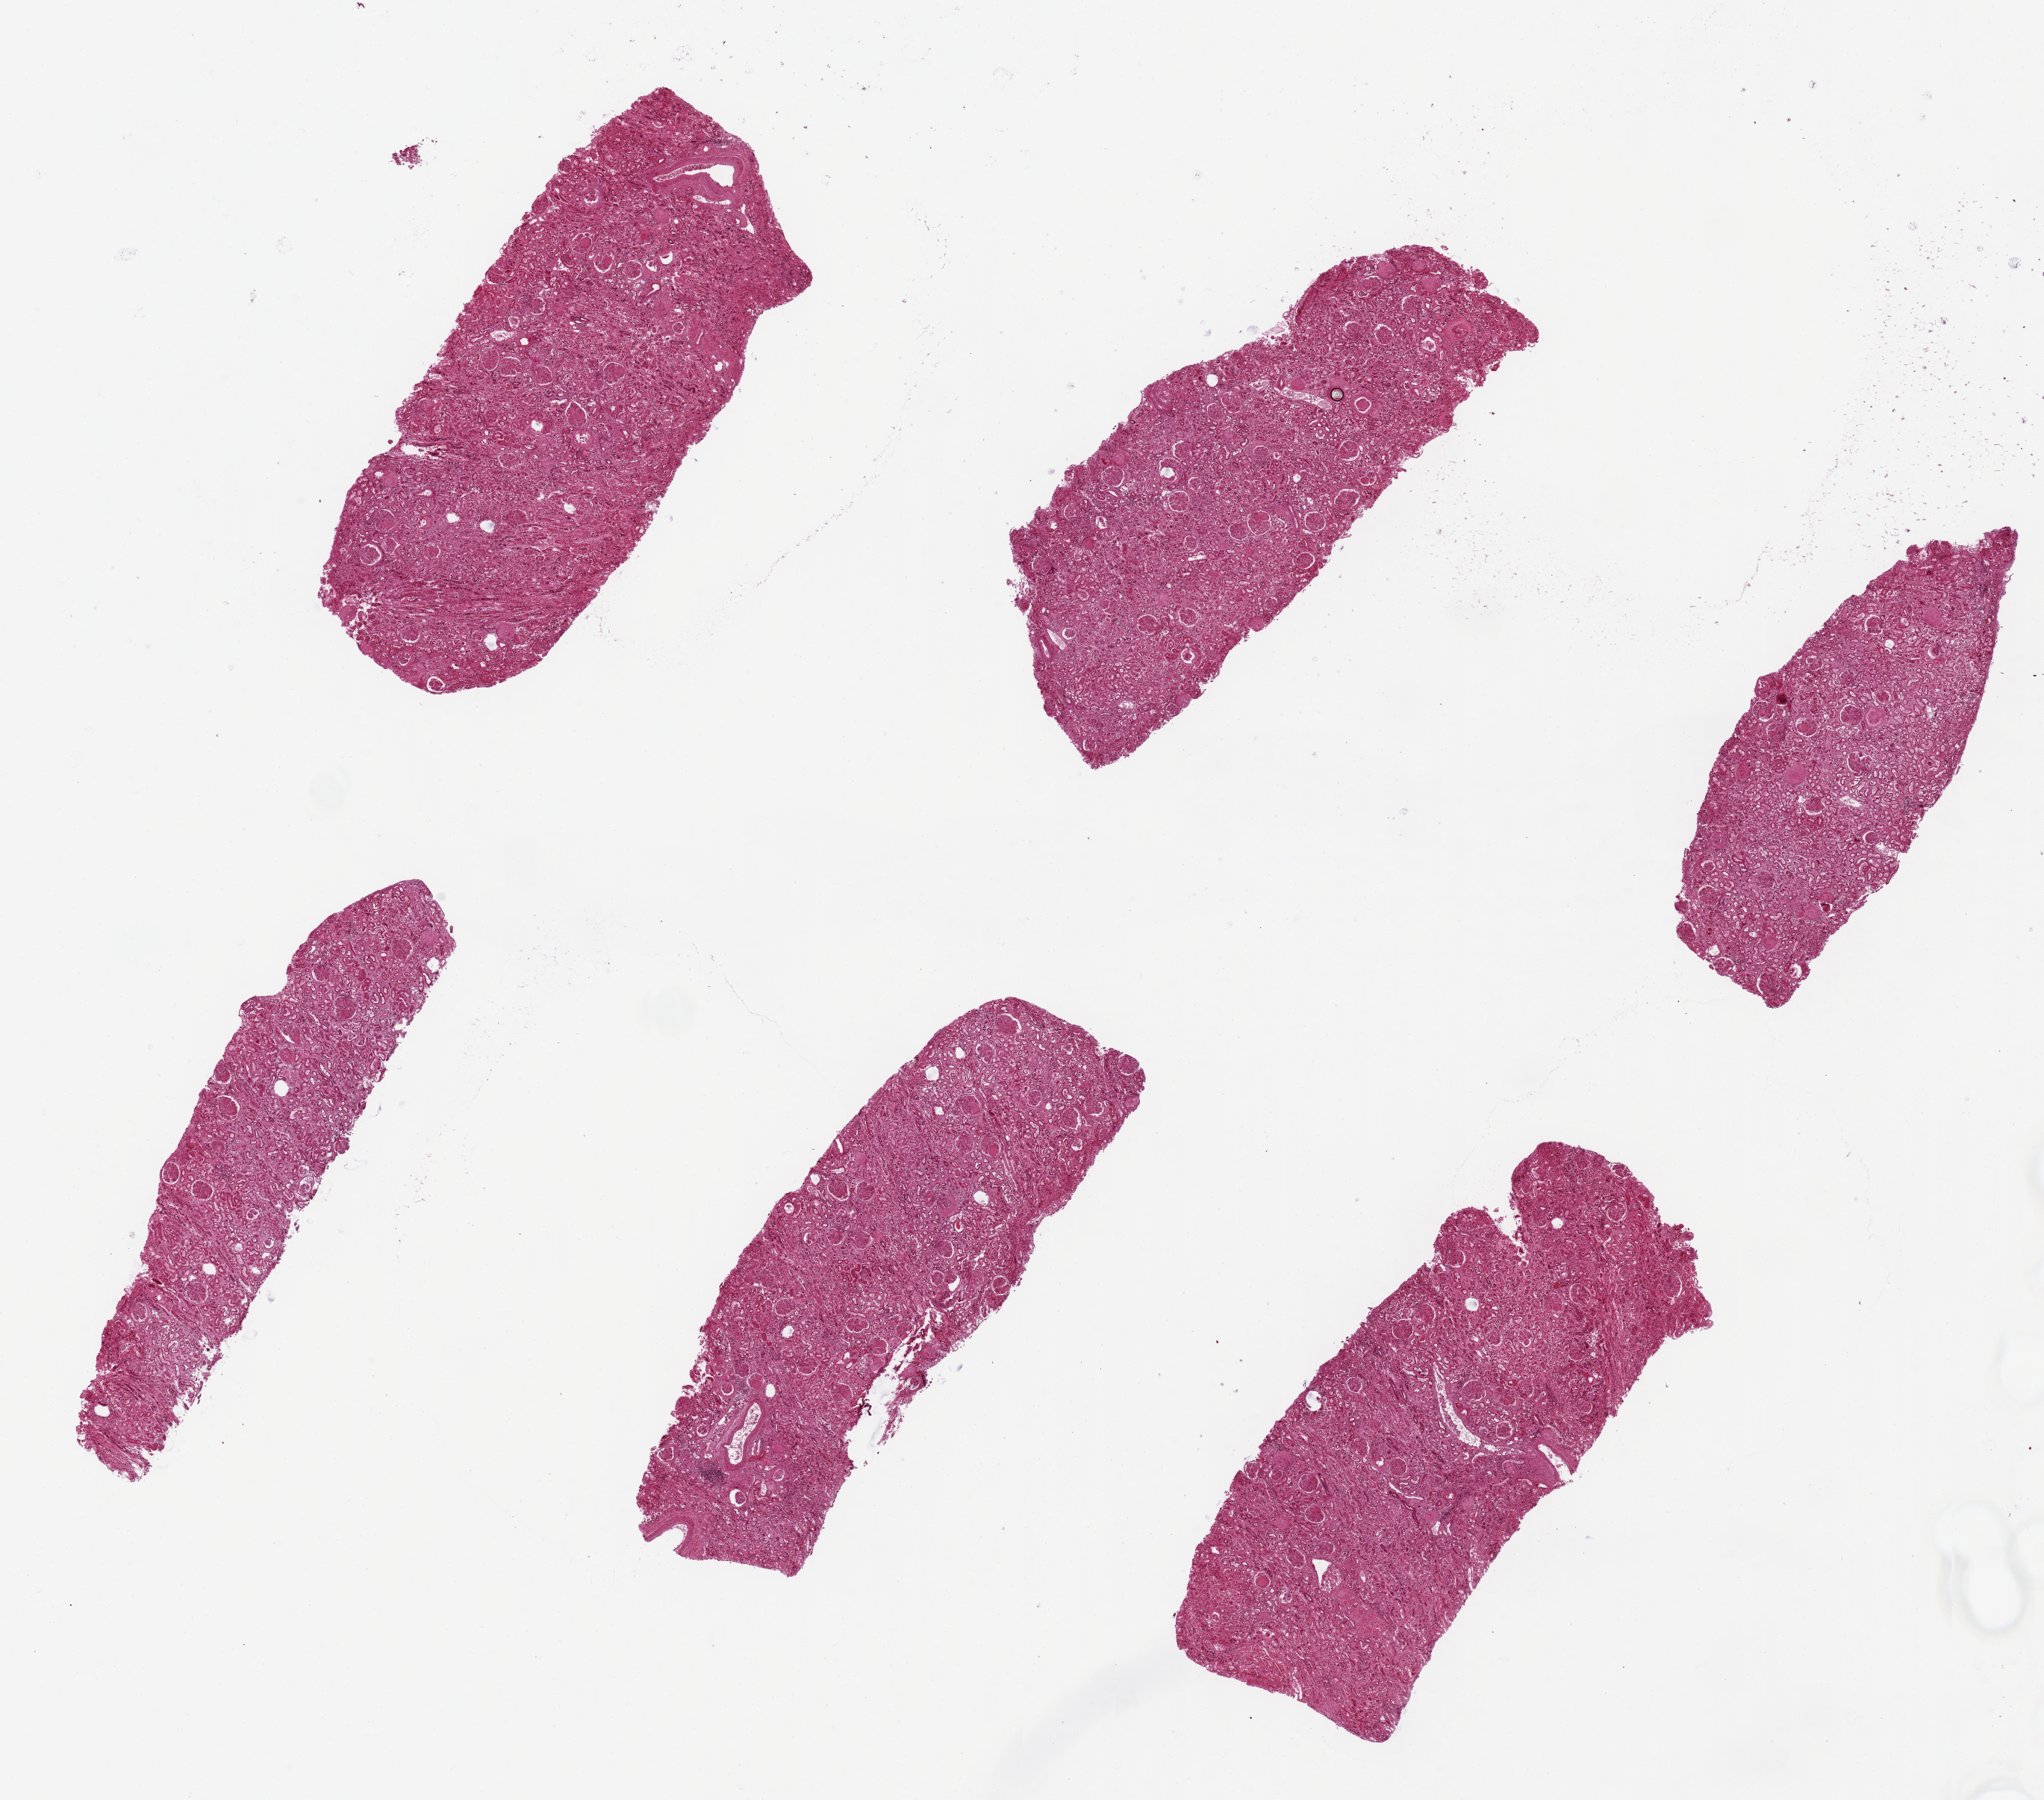
H&E whole-slide image, shown as a low-resolution overview of the whole scanned area (about 21.7 x 19.1 mm). PAXgene-fixed, paraffin-embedded tissue. Section of renal cortex (target tissue). Donor tissue sample.
Review note (as recorded): 6 pieces up to 7x3 mm; virtually all glomeruli are sclerosed, many showing characteristic diabetic glomerulosclerosis; also arterial and arteriolar sclerosis.